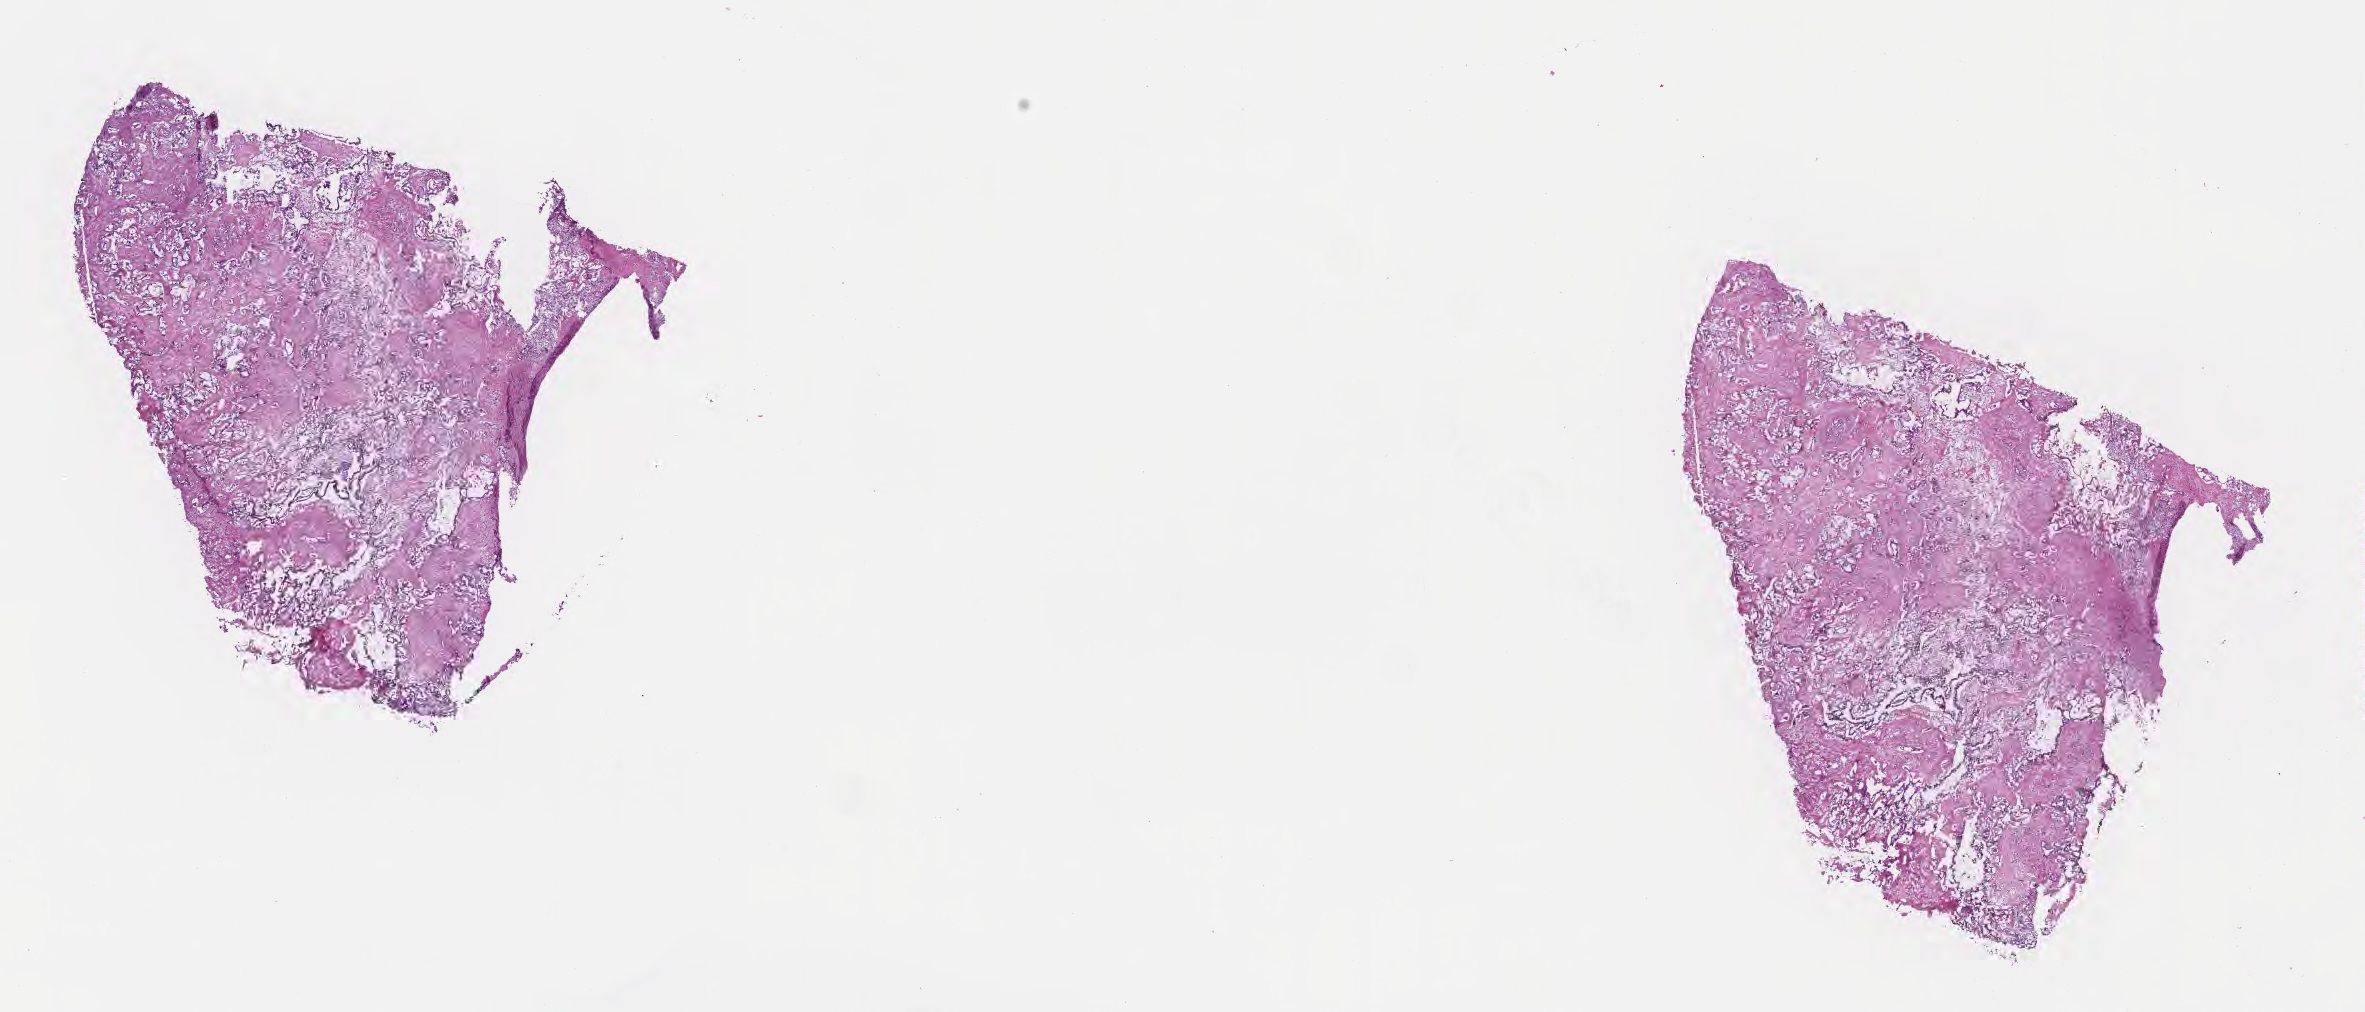
H&E whole-slide image, low-resolution overview of the scanned area, about 19.1 x 8.2 mm; frozen section (tissue freezing medium); specimen: primary tumor; site: extrahepatic bile duct. Male patient; age at initial diagnosis 62 years. Tumor grade: G2 (moderately differentiated). Pathologist review of this section (percent, as recorded): tumor cells 80%, tumor nuclei 80%, stromal cells 20%, necrosis 0%, normal cells 0%. Infiltration values recorded for this section: lymphocyte infiltration 4%, monocyte infiltration 1%, neutrophil infiltration 6%.
• diagnosis: Cholangiocarcinoma
• AJCC pathologic stage: Stage IV
• section: bottom of the tissue portion